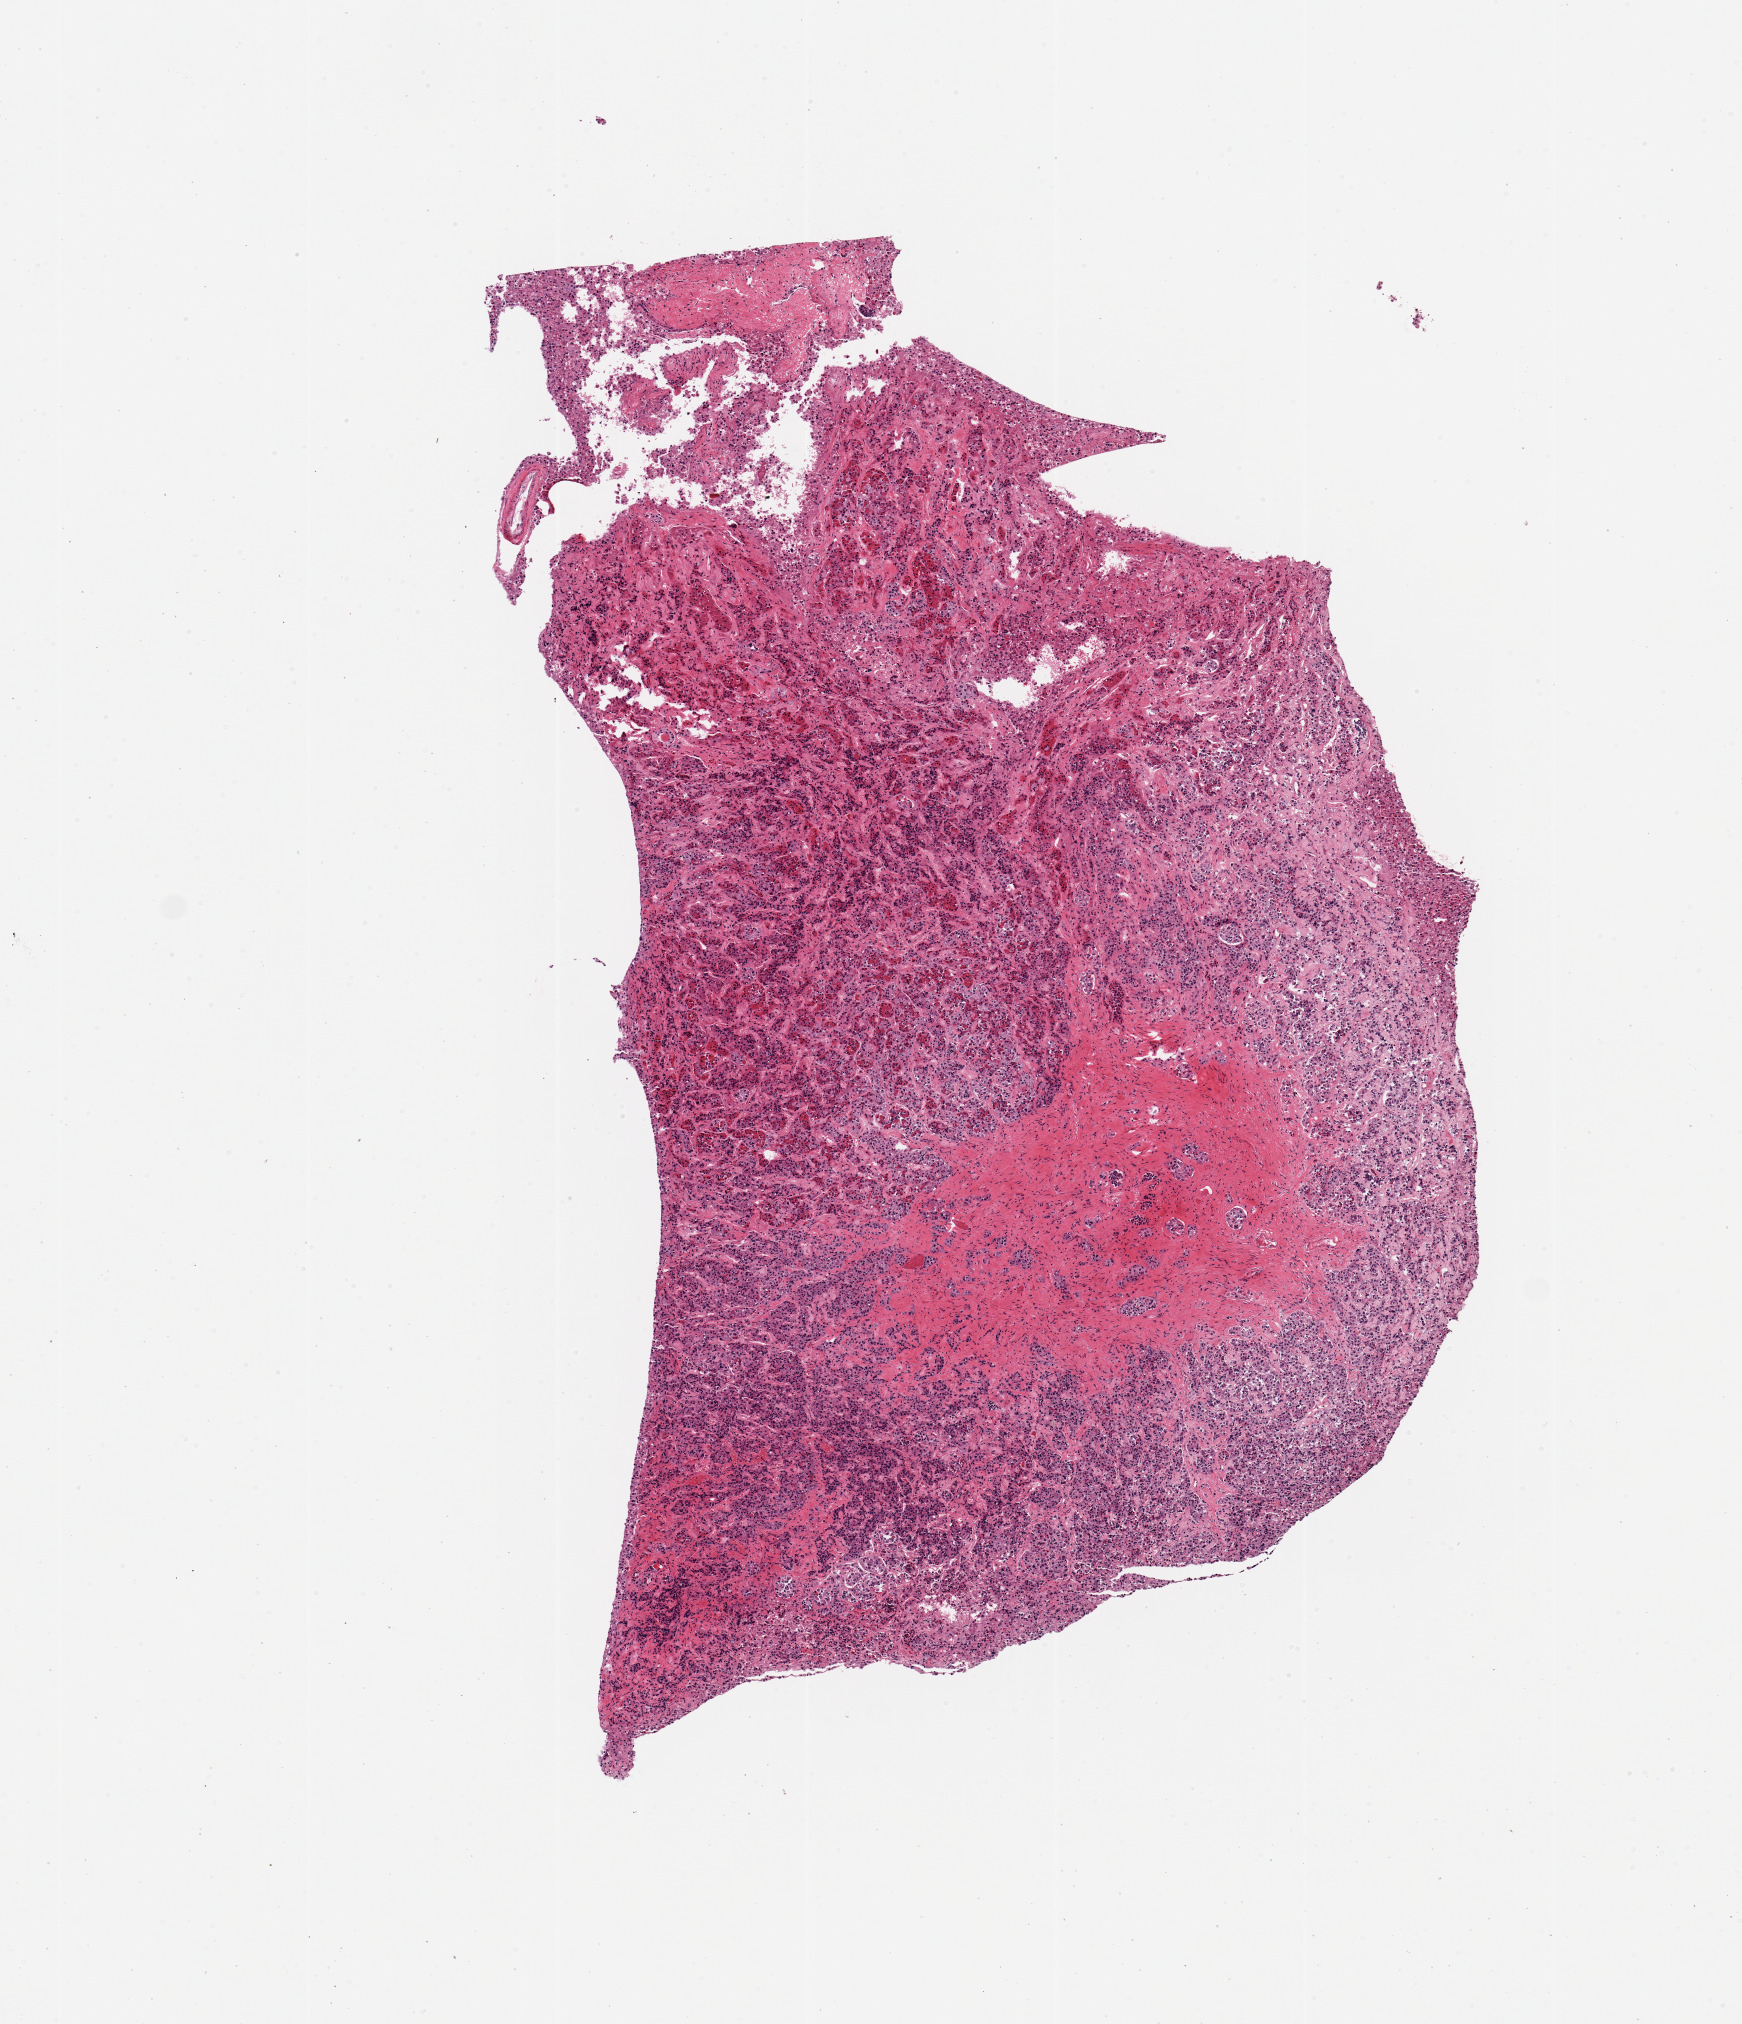
H&E whole-slide image — a low-resolution overview of the entire scanned area, about 6.9 x 8.0 mm; PAXgene-fixed paraffin-embedded (PFPE) section; target tissue: pituitary; donor tissue sample. Male donor.
• reviewer comment on this tissue sample: 1 piece